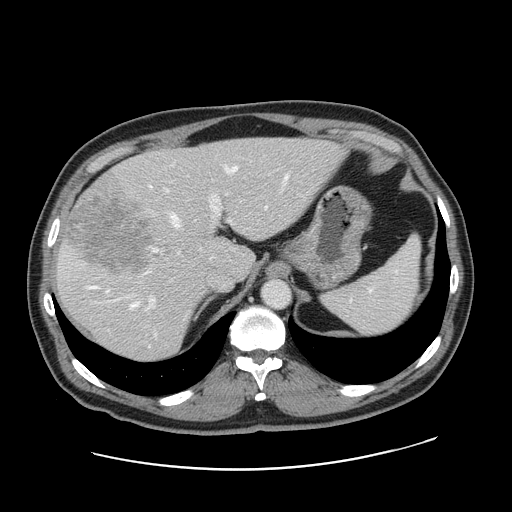
Contrast-enhanced abdominal CT, one axial slice; position 118 of 178 along the scan axis; intravenous contrast given; soft-tissue window (W 400 / L 40 HU); 2.5 mm slice thickness; 512 × 512 image matrix. Male patient, age 63 years. Case-level facts recorded for this patient, not image findings: diagnosis: colorectal cancer liver metastases, imaged before liver resection; multiple liver metastases: yes; largest metastasis: 8 cm.
Annotated regions visible in this slice (expert manual segmentation):
- hepatic veins: bounding box (x1, y1, x2, y2) in pixels: (88, 166, 288, 307)
- liver: (56, 139, 343, 362)
- planned liver remnant (the part of the liver to remain after resection): (140, 139, 344, 278)
- portal vein (with intrahepatic branches): (146, 188, 234, 335)
- liver metastasis: (66, 192, 152, 273)